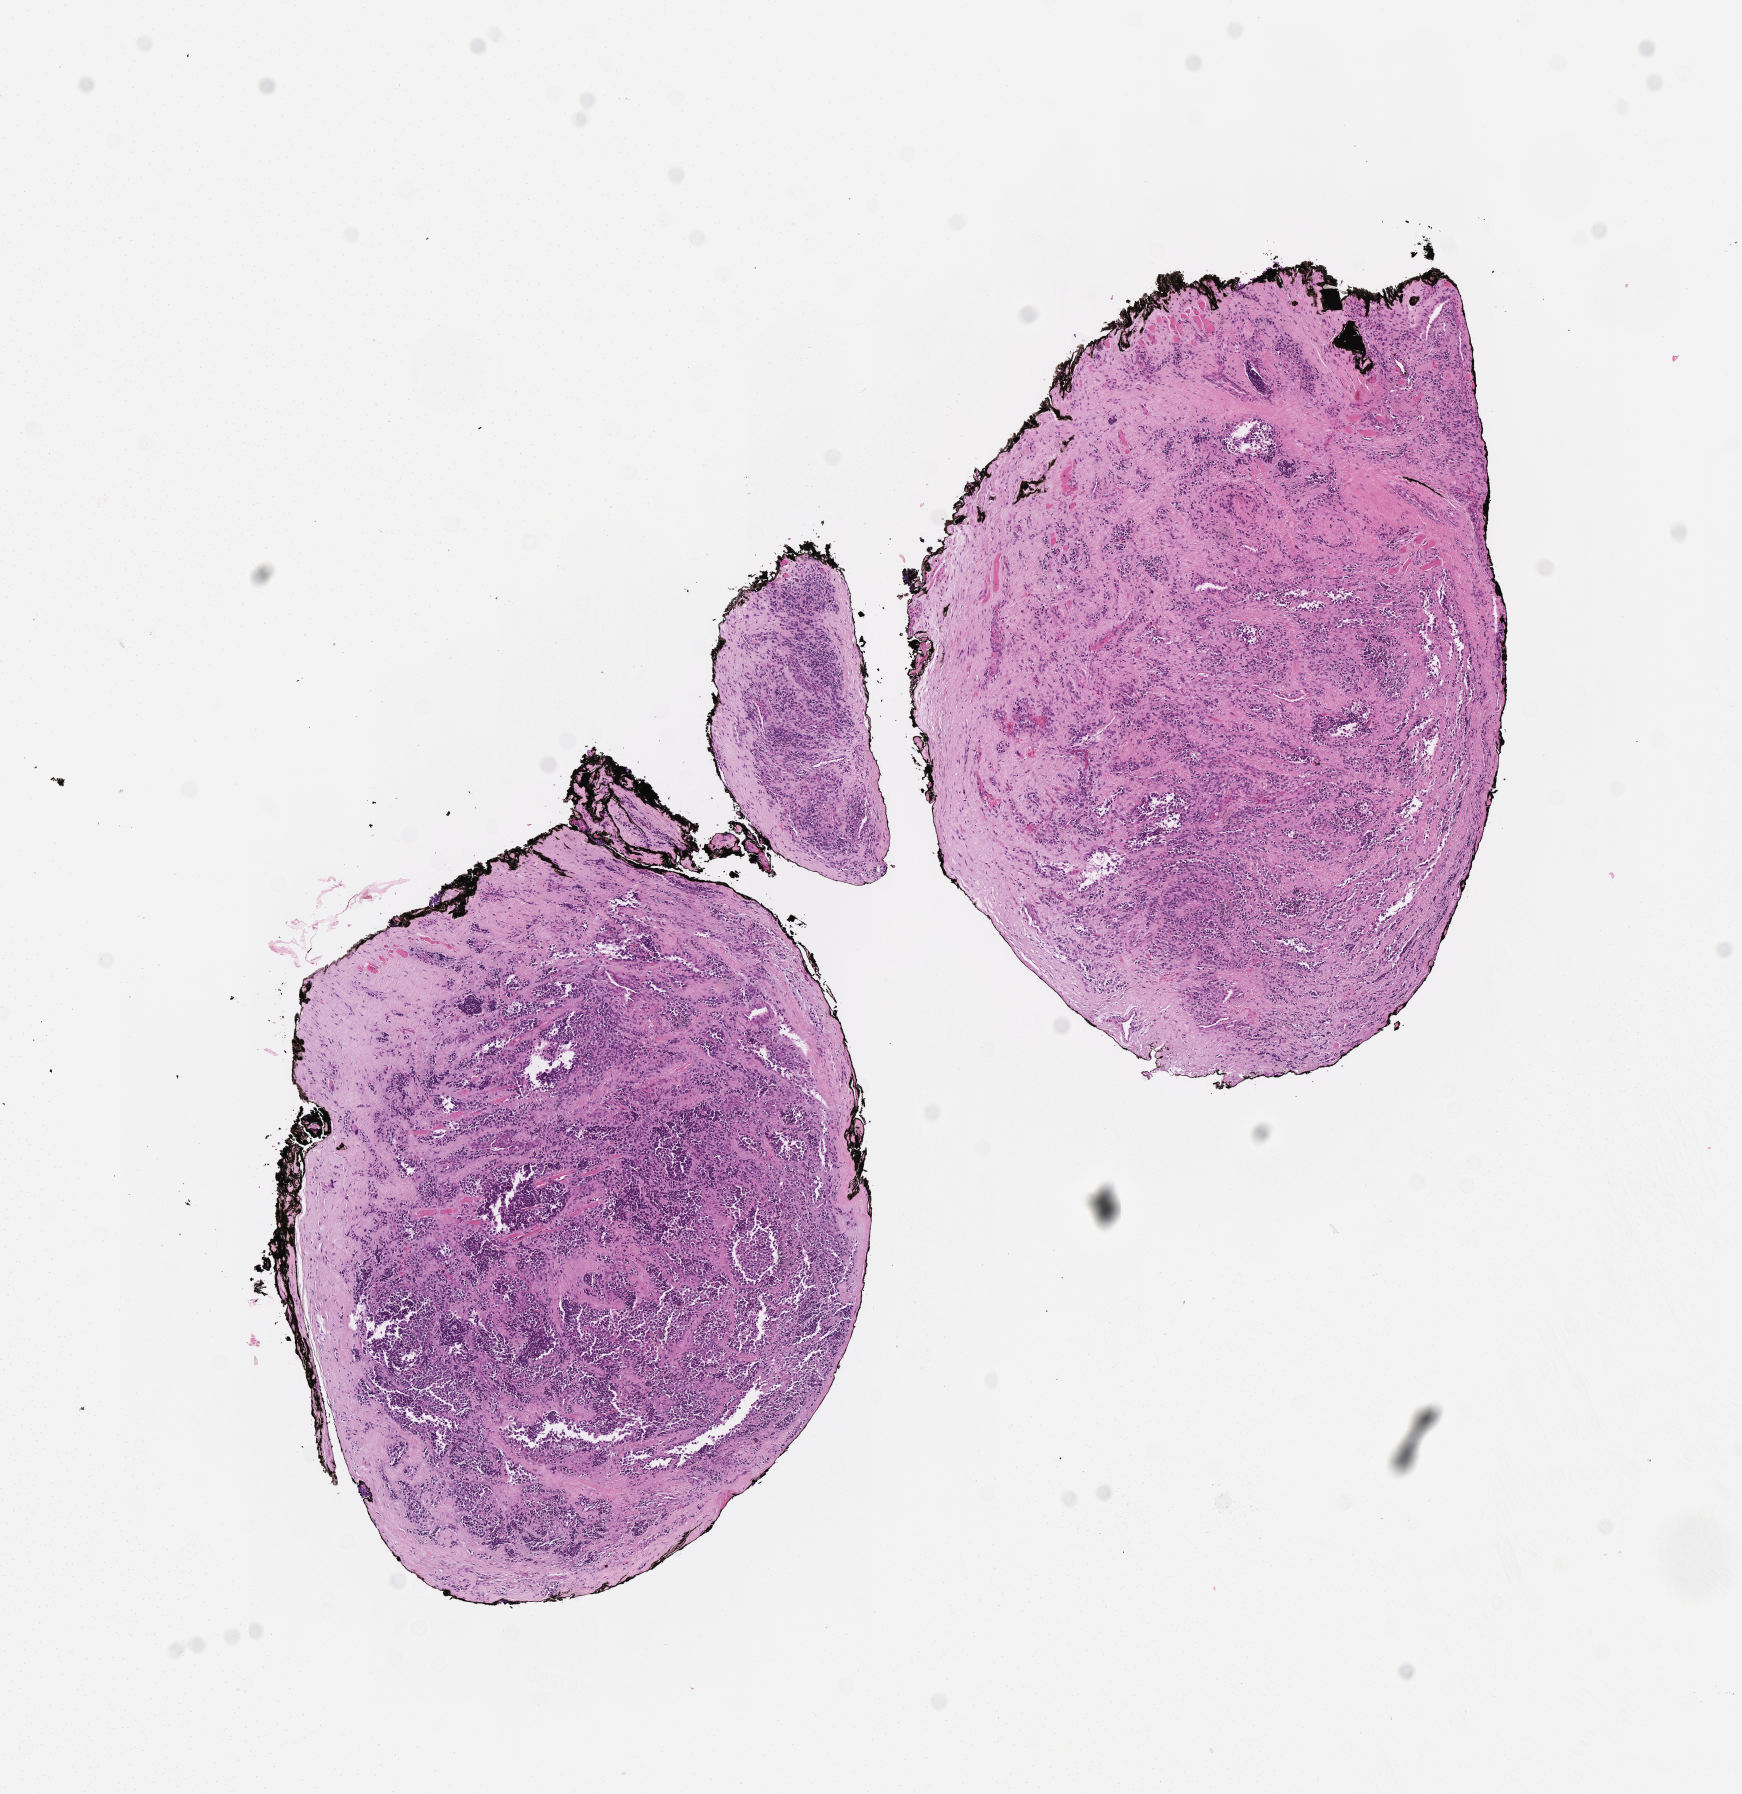
Whole-slide image, hematoxylin and eosin (H&E) stain of tumor tissue — shown as a low-resolution overview of the whole scanned area (about 7.0 x 7.3 mm), FFPE section, site: elbow, left. Male patient, age at diagnosis 1.5 years.
- diagnosis: rhabdomyosarcoma; histological classification: alveolar rhabdomyosarcoma
- stage (as recorded): 2